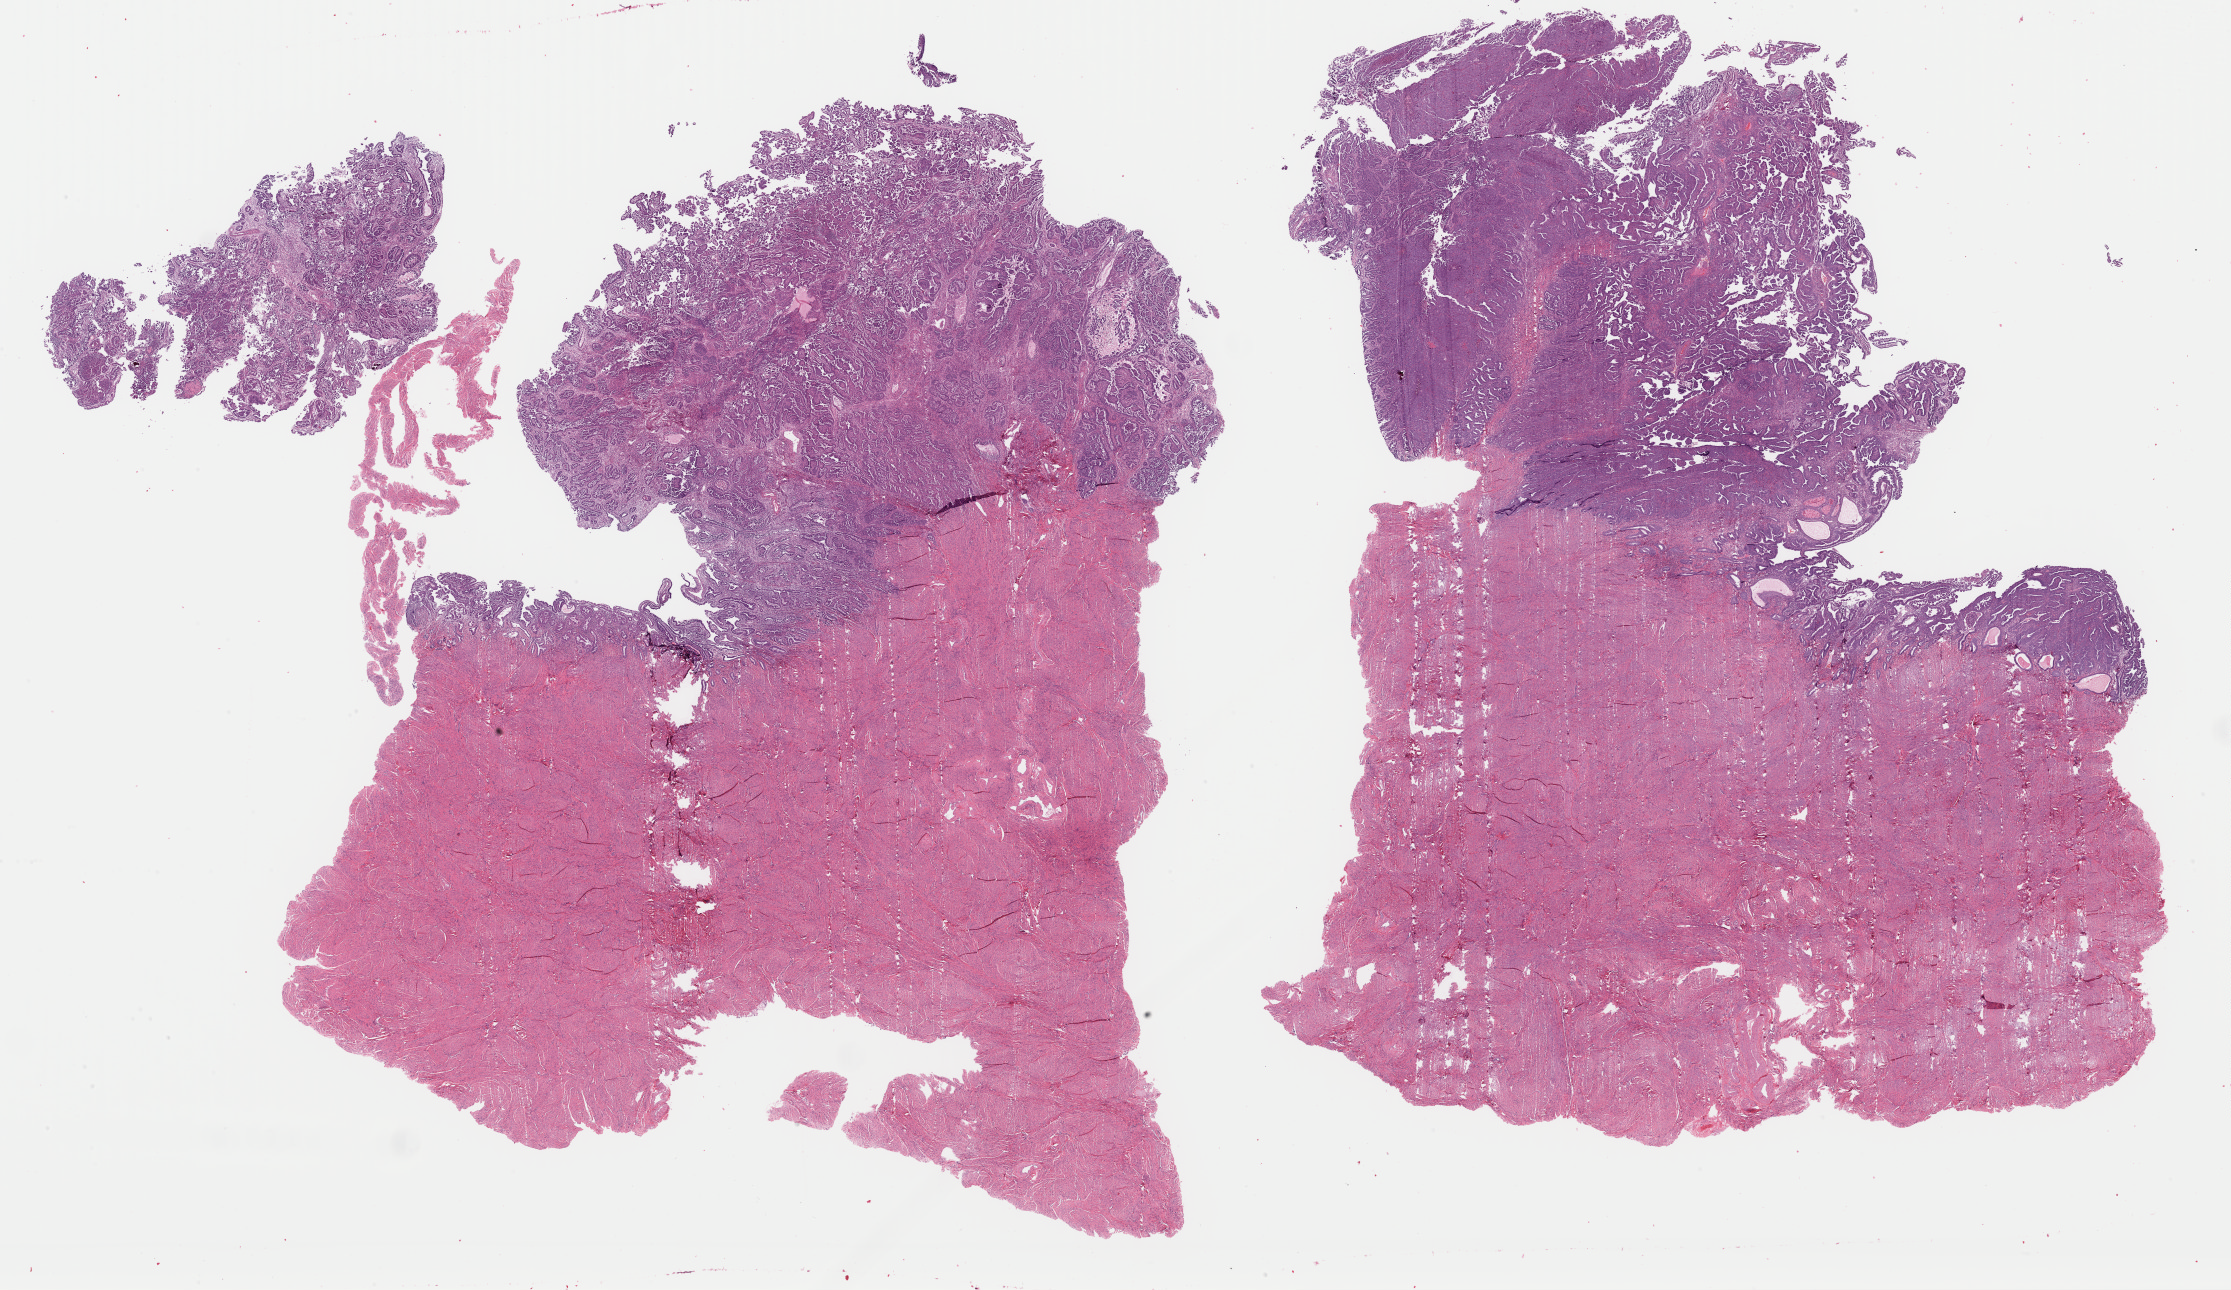
H&E whole-slide image — low-resolution overview of the scanned area, about 35.2 x 20.4 mm. Formalin-fixed paraffin-embedded (FFPE) diagnostic section. Uterus, primary tumour sample. Patient: female, age at initial diagnosis 61 years. Histologic grade: G3 (poorly differentiated).
• pathologic diagnosis: Serous cystadenocarcinoma, NOS (endometrium)
• lymph nodes positive (case pathology): 1 of 28 examined
• FIGO stage: IIIC